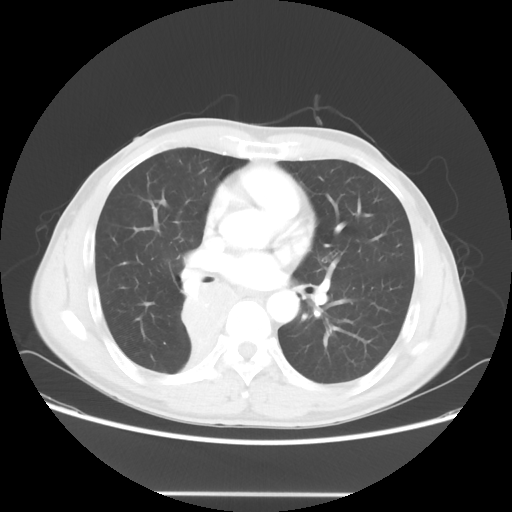
Chest CT, one axial slice. Position 32 of 62 along the scan axis. Reconstruction kernel STANDARD. 120 kVp. Lung window (W 1500 / L -600 HU). 5 mm slice thickness. 512 × 512 image matrix. Male patient, age 47 years. From the clinical record (not read from this slice): clinical TNM (as recorded): T2 N0 M0; histopathological grade: G2.
Structures marked on this image (rectangle marked by the reading radiologist):
- lung tumour (recorded histology: squamous cell carcinoma): bounding box (x1, y1, x2, y2) in pixels: (172, 273, 233, 369)